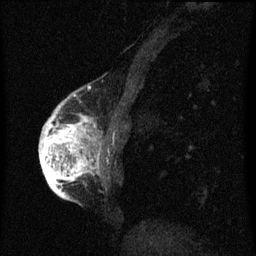
Breast MRI (dynamic contrast-enhanced), one sagittal slice. Position 19 of 60 along the scan axis. Dynamic contrast-enhanced series, image 2 of 3 at this slice position (ordered by acquisition). 1.5 T. TE 4.2 ms, TR 8 ms. 256 × 256 image matrix, field of view 180 × 180 mm. Female patient, age 56 years.
Outlined on this slice (semi-automatic segmentation, software-assisted and operator-edited):
- analysis volume of interest (the breast-tissue region the enhancement analysis was run in; not a lesion): bounding box (x1, y1, x2, y2) in pixels: (42, 110, 103, 193)
- tumour enhancement mask (voxels above the 70 % enhancement threshold inside the analysis volume of interest): (42, 110, 99, 193)